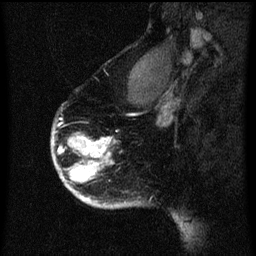
Breast MRI (dynamic contrast-enhanced), one sagittal slice. Position 49 of 60 along the scan axis. Dynamic contrast-enhanced series, image 2 of 3 at this slice position (ordered by acquisition). 1.5 T. TE 4.2 ms, TR 8 ms. 2 mm slice thickness. 256 × 256 image matrix. Female patient, age 56 years.
Structures marked on this image (semi-automatically segmented with operator editing):
- analysis volume of interest (the breast-tissue region the enhancement analysis was run in; not a lesion): box from (x=52, y=104) to (x=125, y=209) px
- tumour enhancement mask (voxels above the 70 % enhancement threshold inside the analysis volume of interest): (x=52, y=138)–(x=119, y=207)